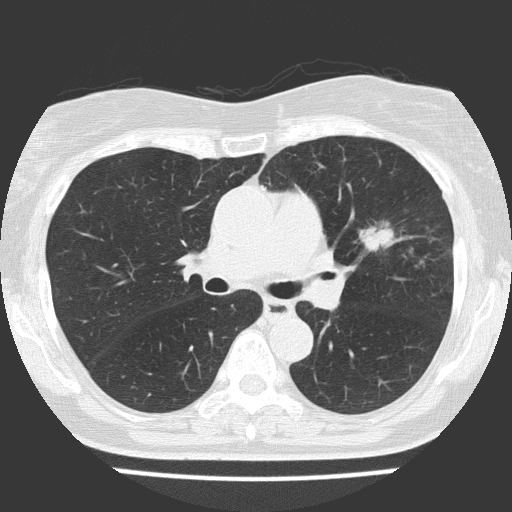
Axial slice from a low-dose chest CT screening exam, baseline screening round, lung window (W 1500 / L -600 HU), 2 mm slice thickness, 512 × 512 image matrix. Female participant, aged 70 years at enrolment. Current smoker at enrolment.
Lesion marked by an expert reader, box from (x=327, y=195) to (x=432, y=284) px. The screening reader recorded 2 non-calcified nodules or masses ≥4 mm on this exam; which of them this box marks is not recorded. Participant outcome: lung cancer diagnosed 25 days after this screen — adenocarcinoma, NOS, left upper lobe, poorly differentiated (G3), stage IV (AJCC 6th edition), 30 mm at pathology.